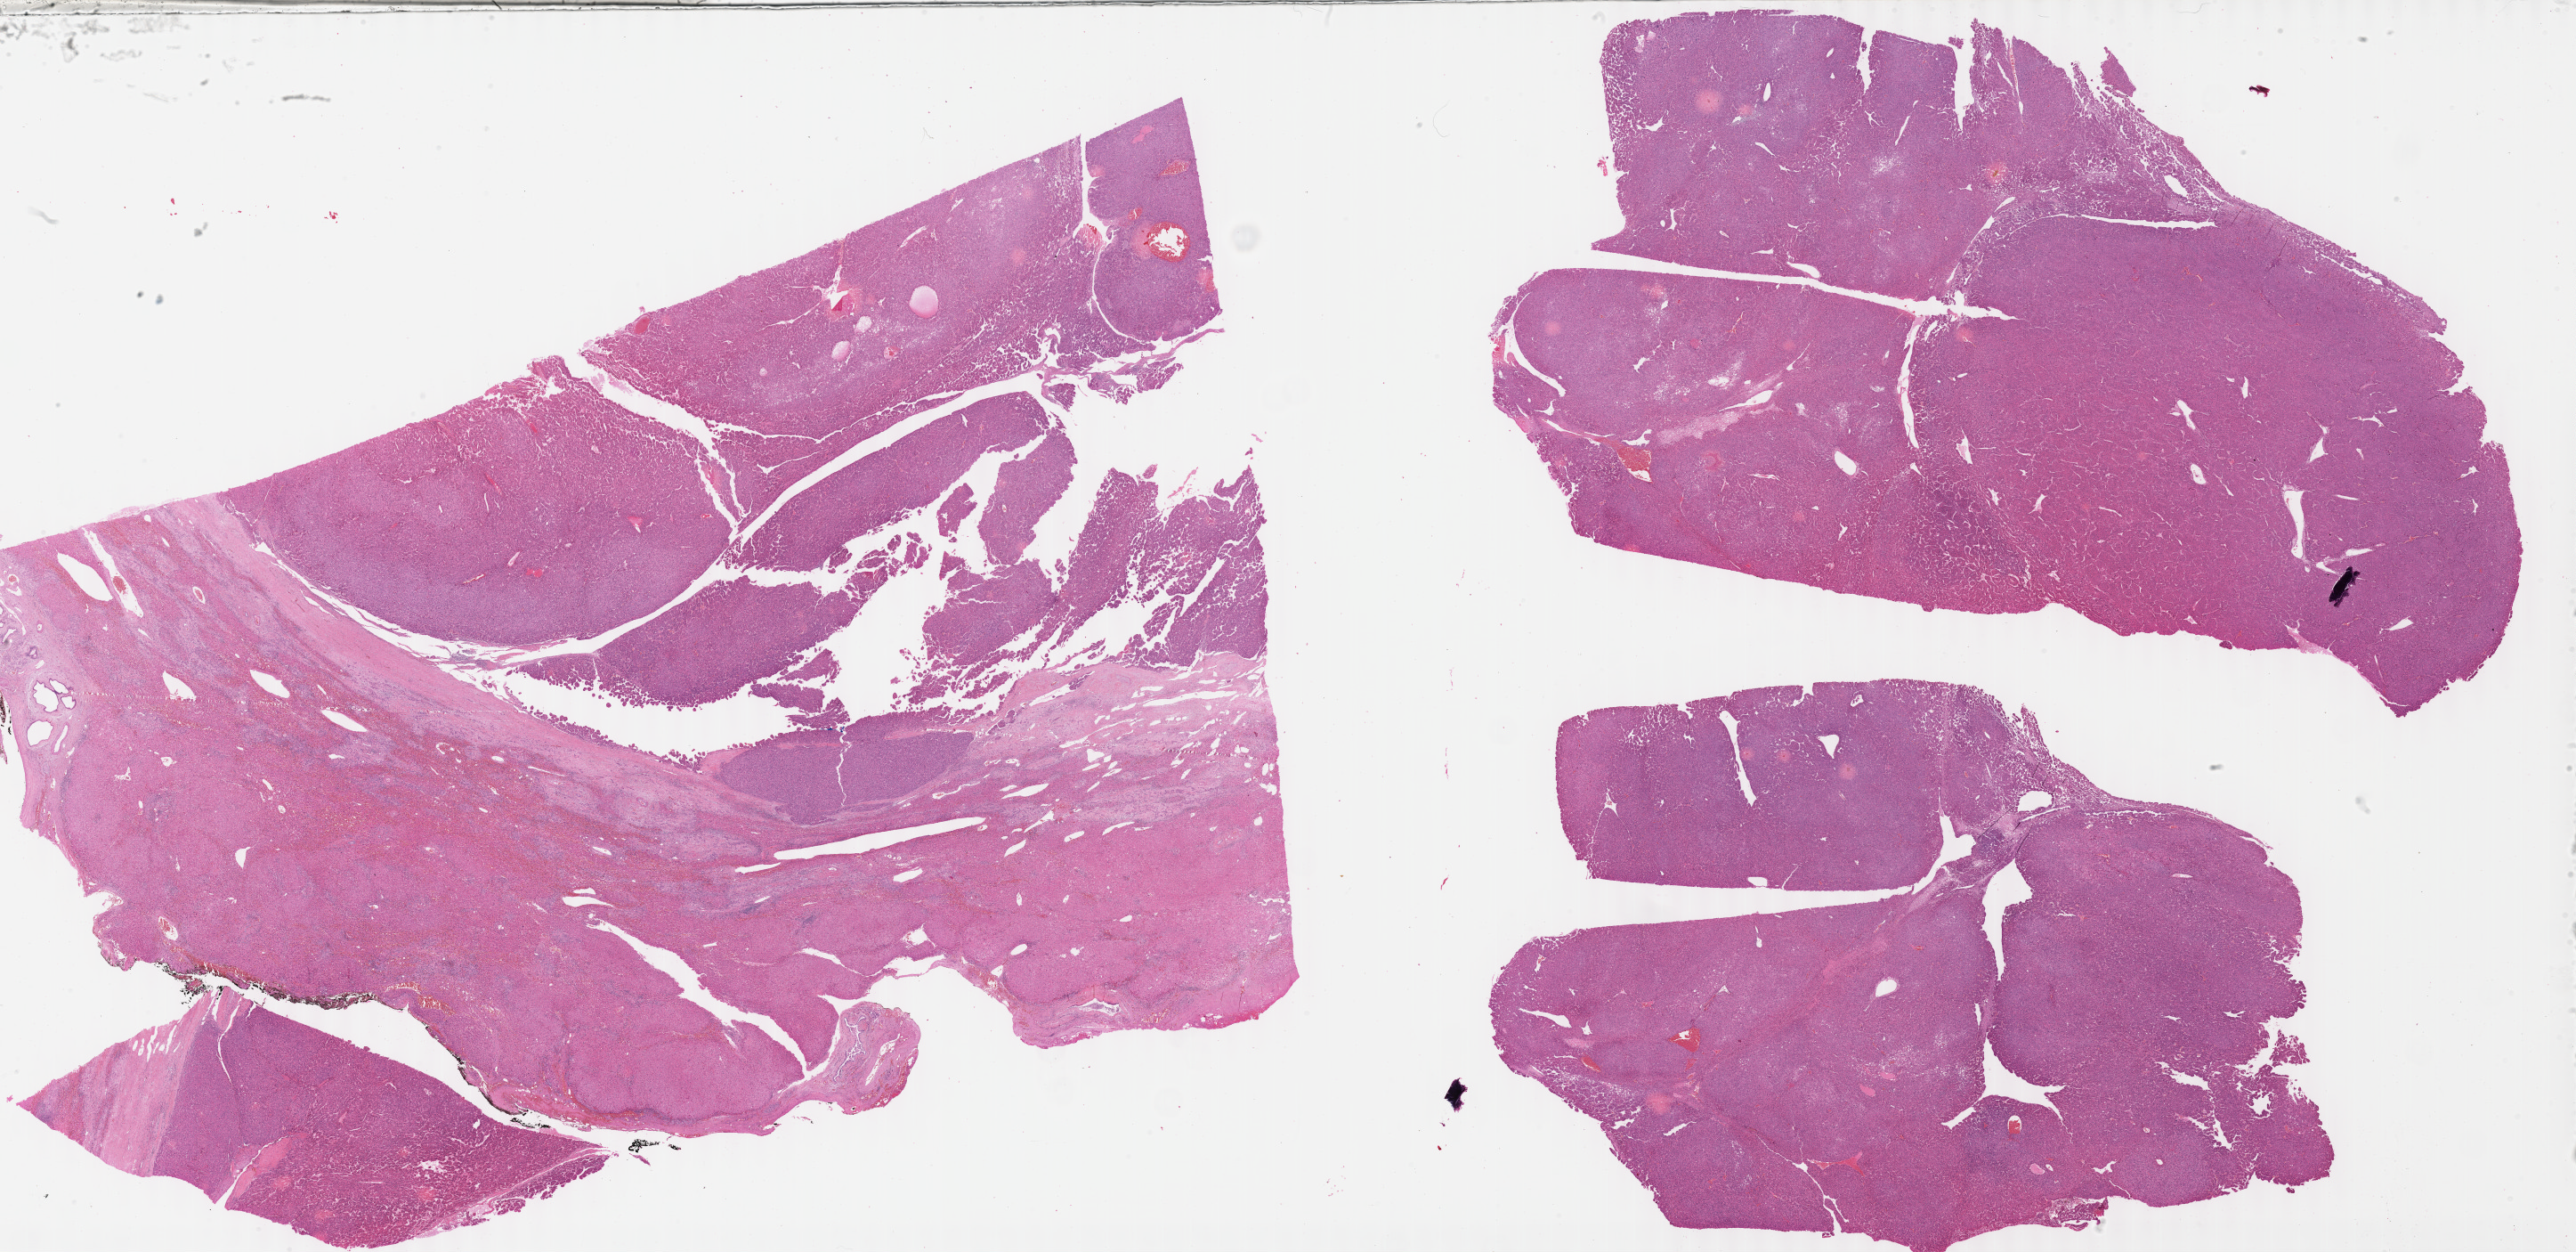
Hematoxylin and eosin (H&E) stained whole-slide image — low-resolution overview of the scanned area, about 46.8 x 22.7 mm (acquisition: 40x scan), formalin-fixed paraffin-embedded (FFPE) diagnostic section, liver, primary tumour sample. Patient: male, age at initial diagnosis 74 years.
Pathologic diagnosis: Hepatocellular carcinoma, NOS.